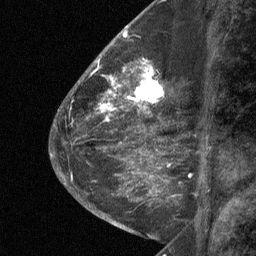
Breast MRI (dynamic contrast-enhanced), one sagittal slice. Position 25 of 64 along the scan axis. Dynamic contrast-enhanced study with each time point stored as its own series, time point 2 of 3 at this slice position (early post-contrast, ordered by acquisition time). 1.5 T. TE 4.8 ms, TR 27 ms. 2 mm slice thickness. 256 × 256 image matrix, field of view 180 × 180 mm. Female patient, age 59 years. From the clinical record (not read from this slice): setting: breast cancer imaged before/during neoadjuvant chemotherapy; receptor status: triple-negative.
Outlined on this slice (semi-automatically segmented with operator editing):
- analysis volume of interest (the breast-tissue region the enhancement analysis was run in; not a lesion): box from (x=122, y=59) to (x=176, y=109) px
- tumour enhancement mask (voxels above the 90 % enhancement threshold inside the analysis volume of interest): (x=127, y=59)–(x=164, y=108)